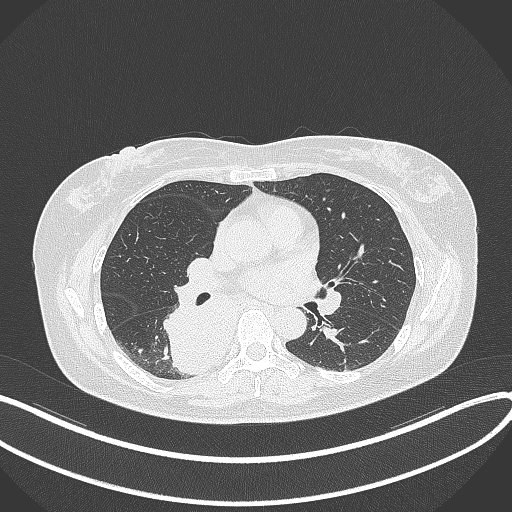
Chest CT, one axial slice; slice 194 of 331 in the series (ordered by position); reconstruction kernel B70f; lung window (W 1500 / L -600 HU); 1 mm slice thickness; 512 × 512 image matrix, field of view 400 × 400 mm. Patient: female, 54 years. From the clinical record (not read from this slice): clinical TNM (as recorded): T4 N0 M0.
Outlined on this slice (rectangle marked by the reading radiologist):
- lung tumour (recorded histology: adenocarcinoma): bounding box [x1, y1, x2, y2] px = [164, 294, 240, 378]